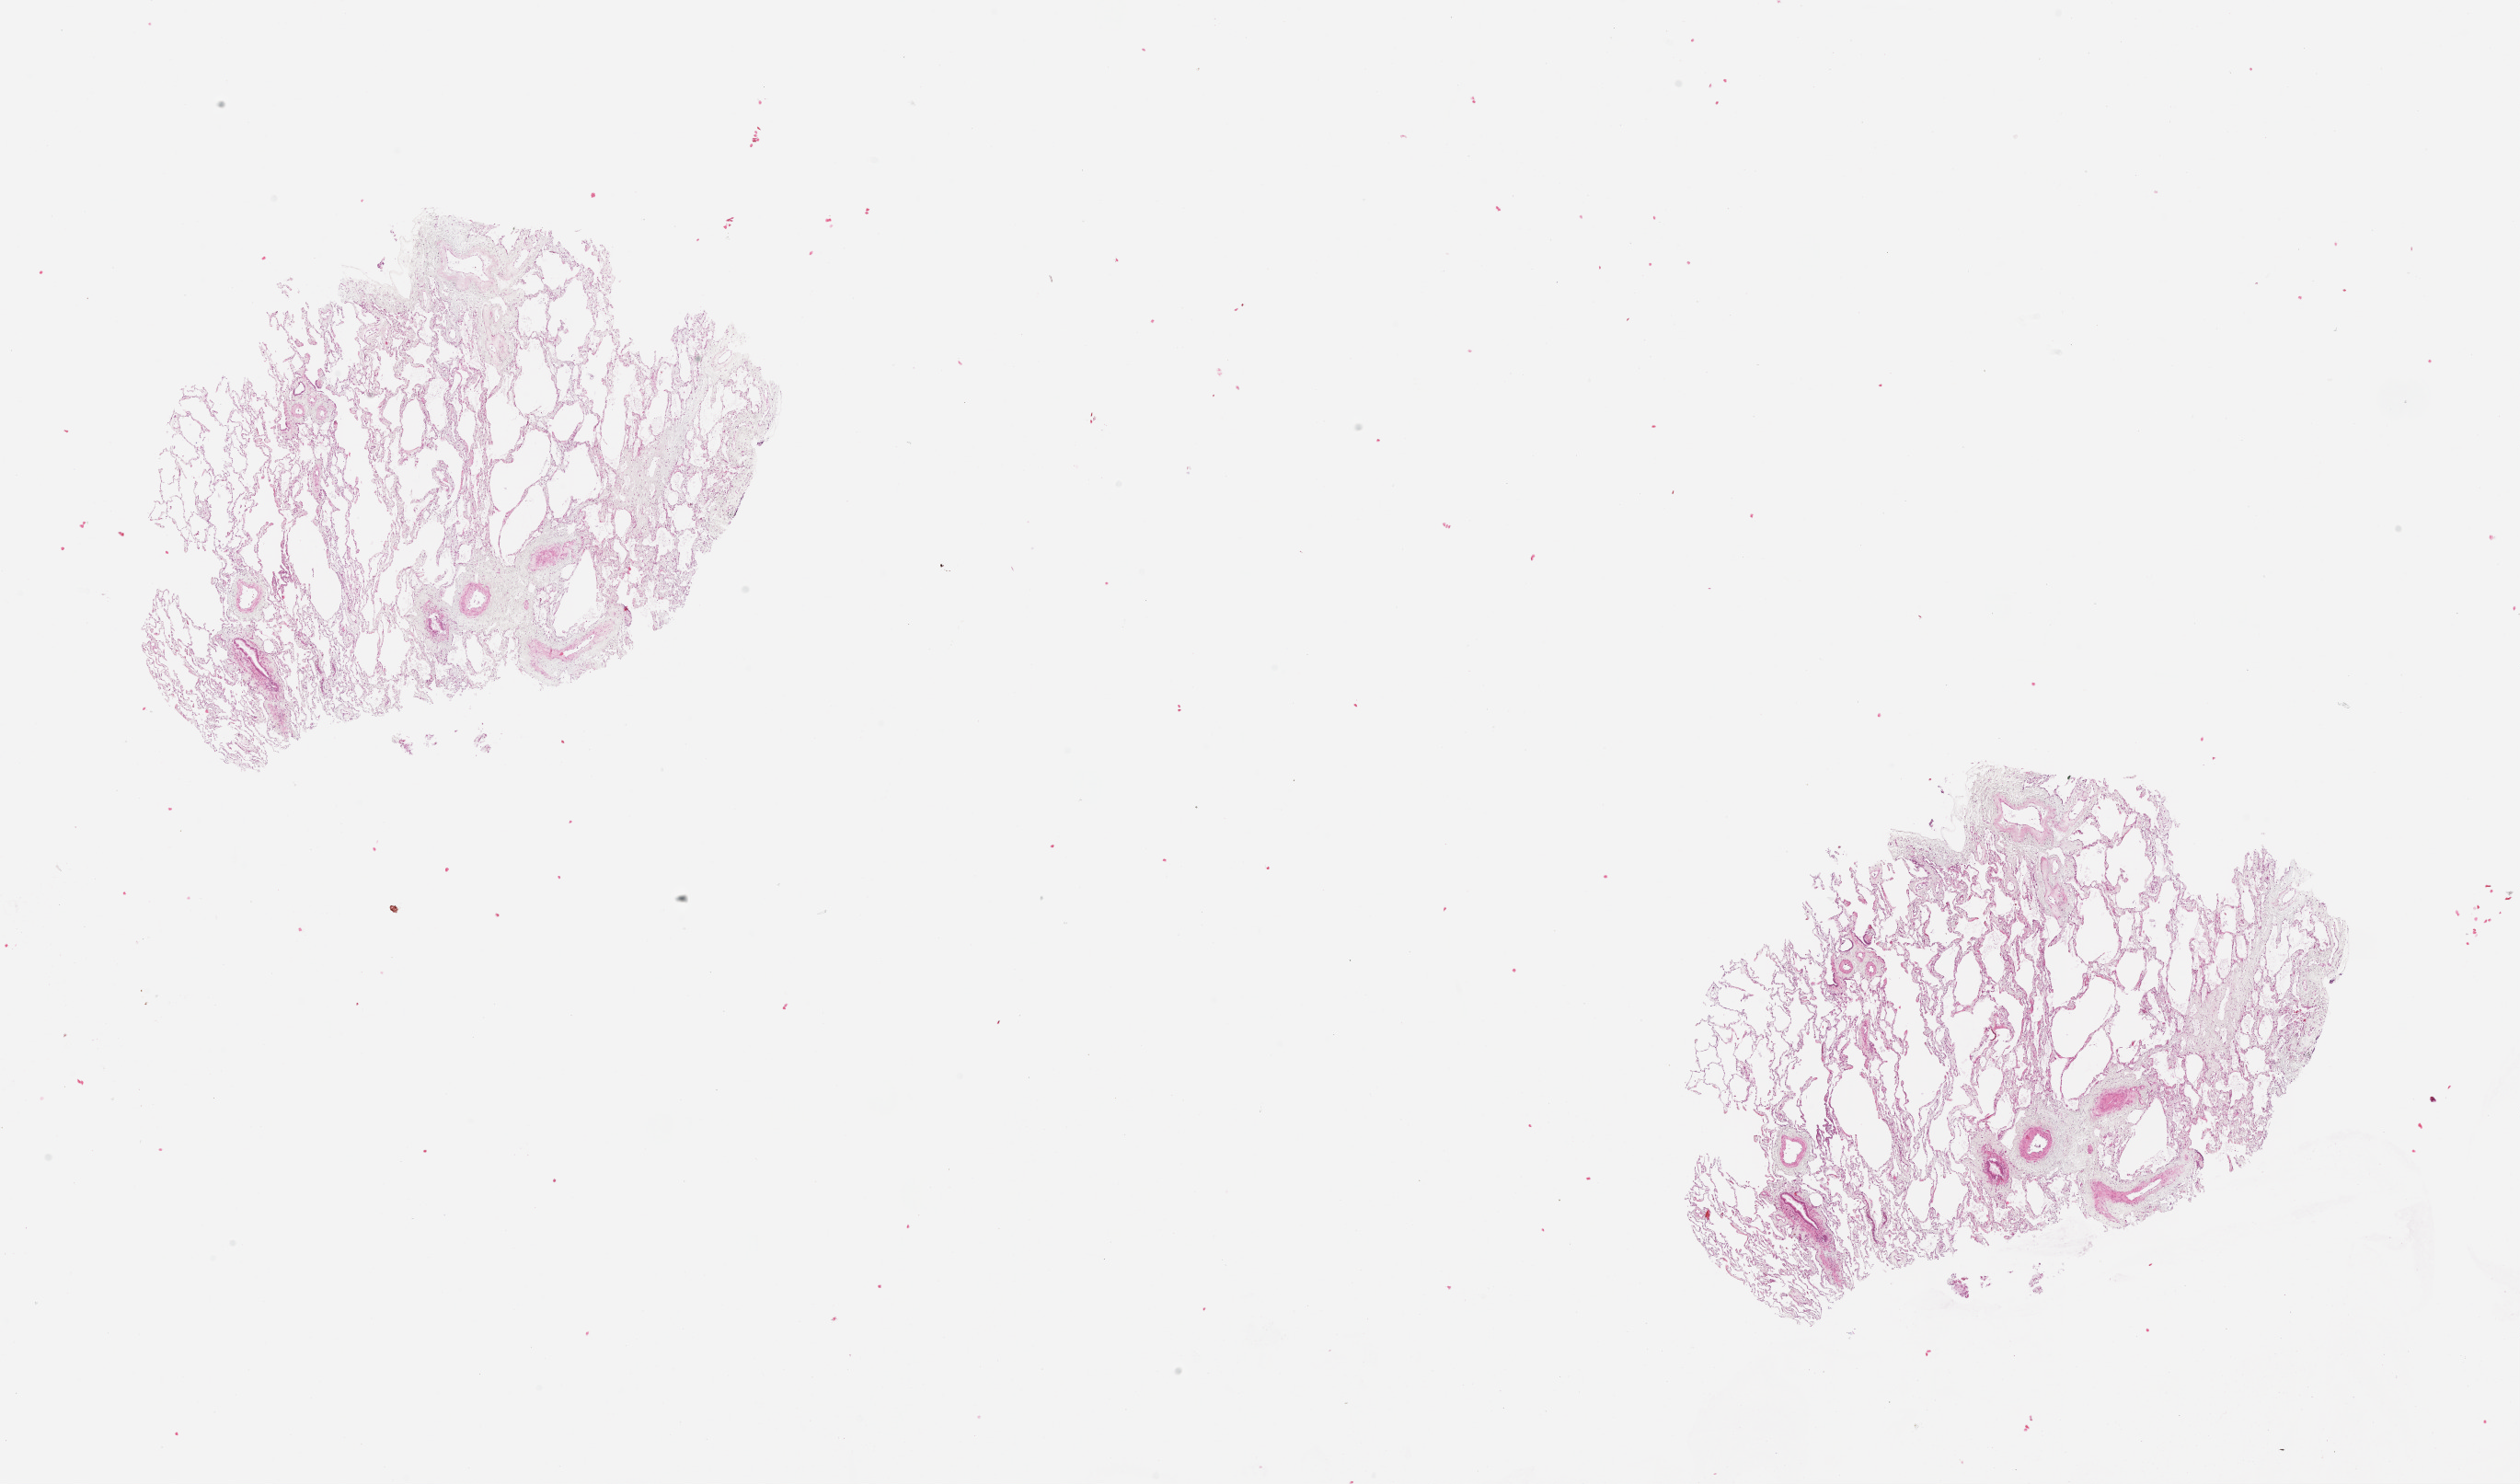
Whole-slide histology image, H&E — low-resolution overview of the scanned area, about 22.0 x 13.0 mm (from a 20x scan); lung, normal (non-tumour) tissue. Patient: female, age 66 years.
This section: normal (non-tumour) tissue from the same patient. Patient diagnosis (cohort enrolment): squamous cell carcinoma (lung).